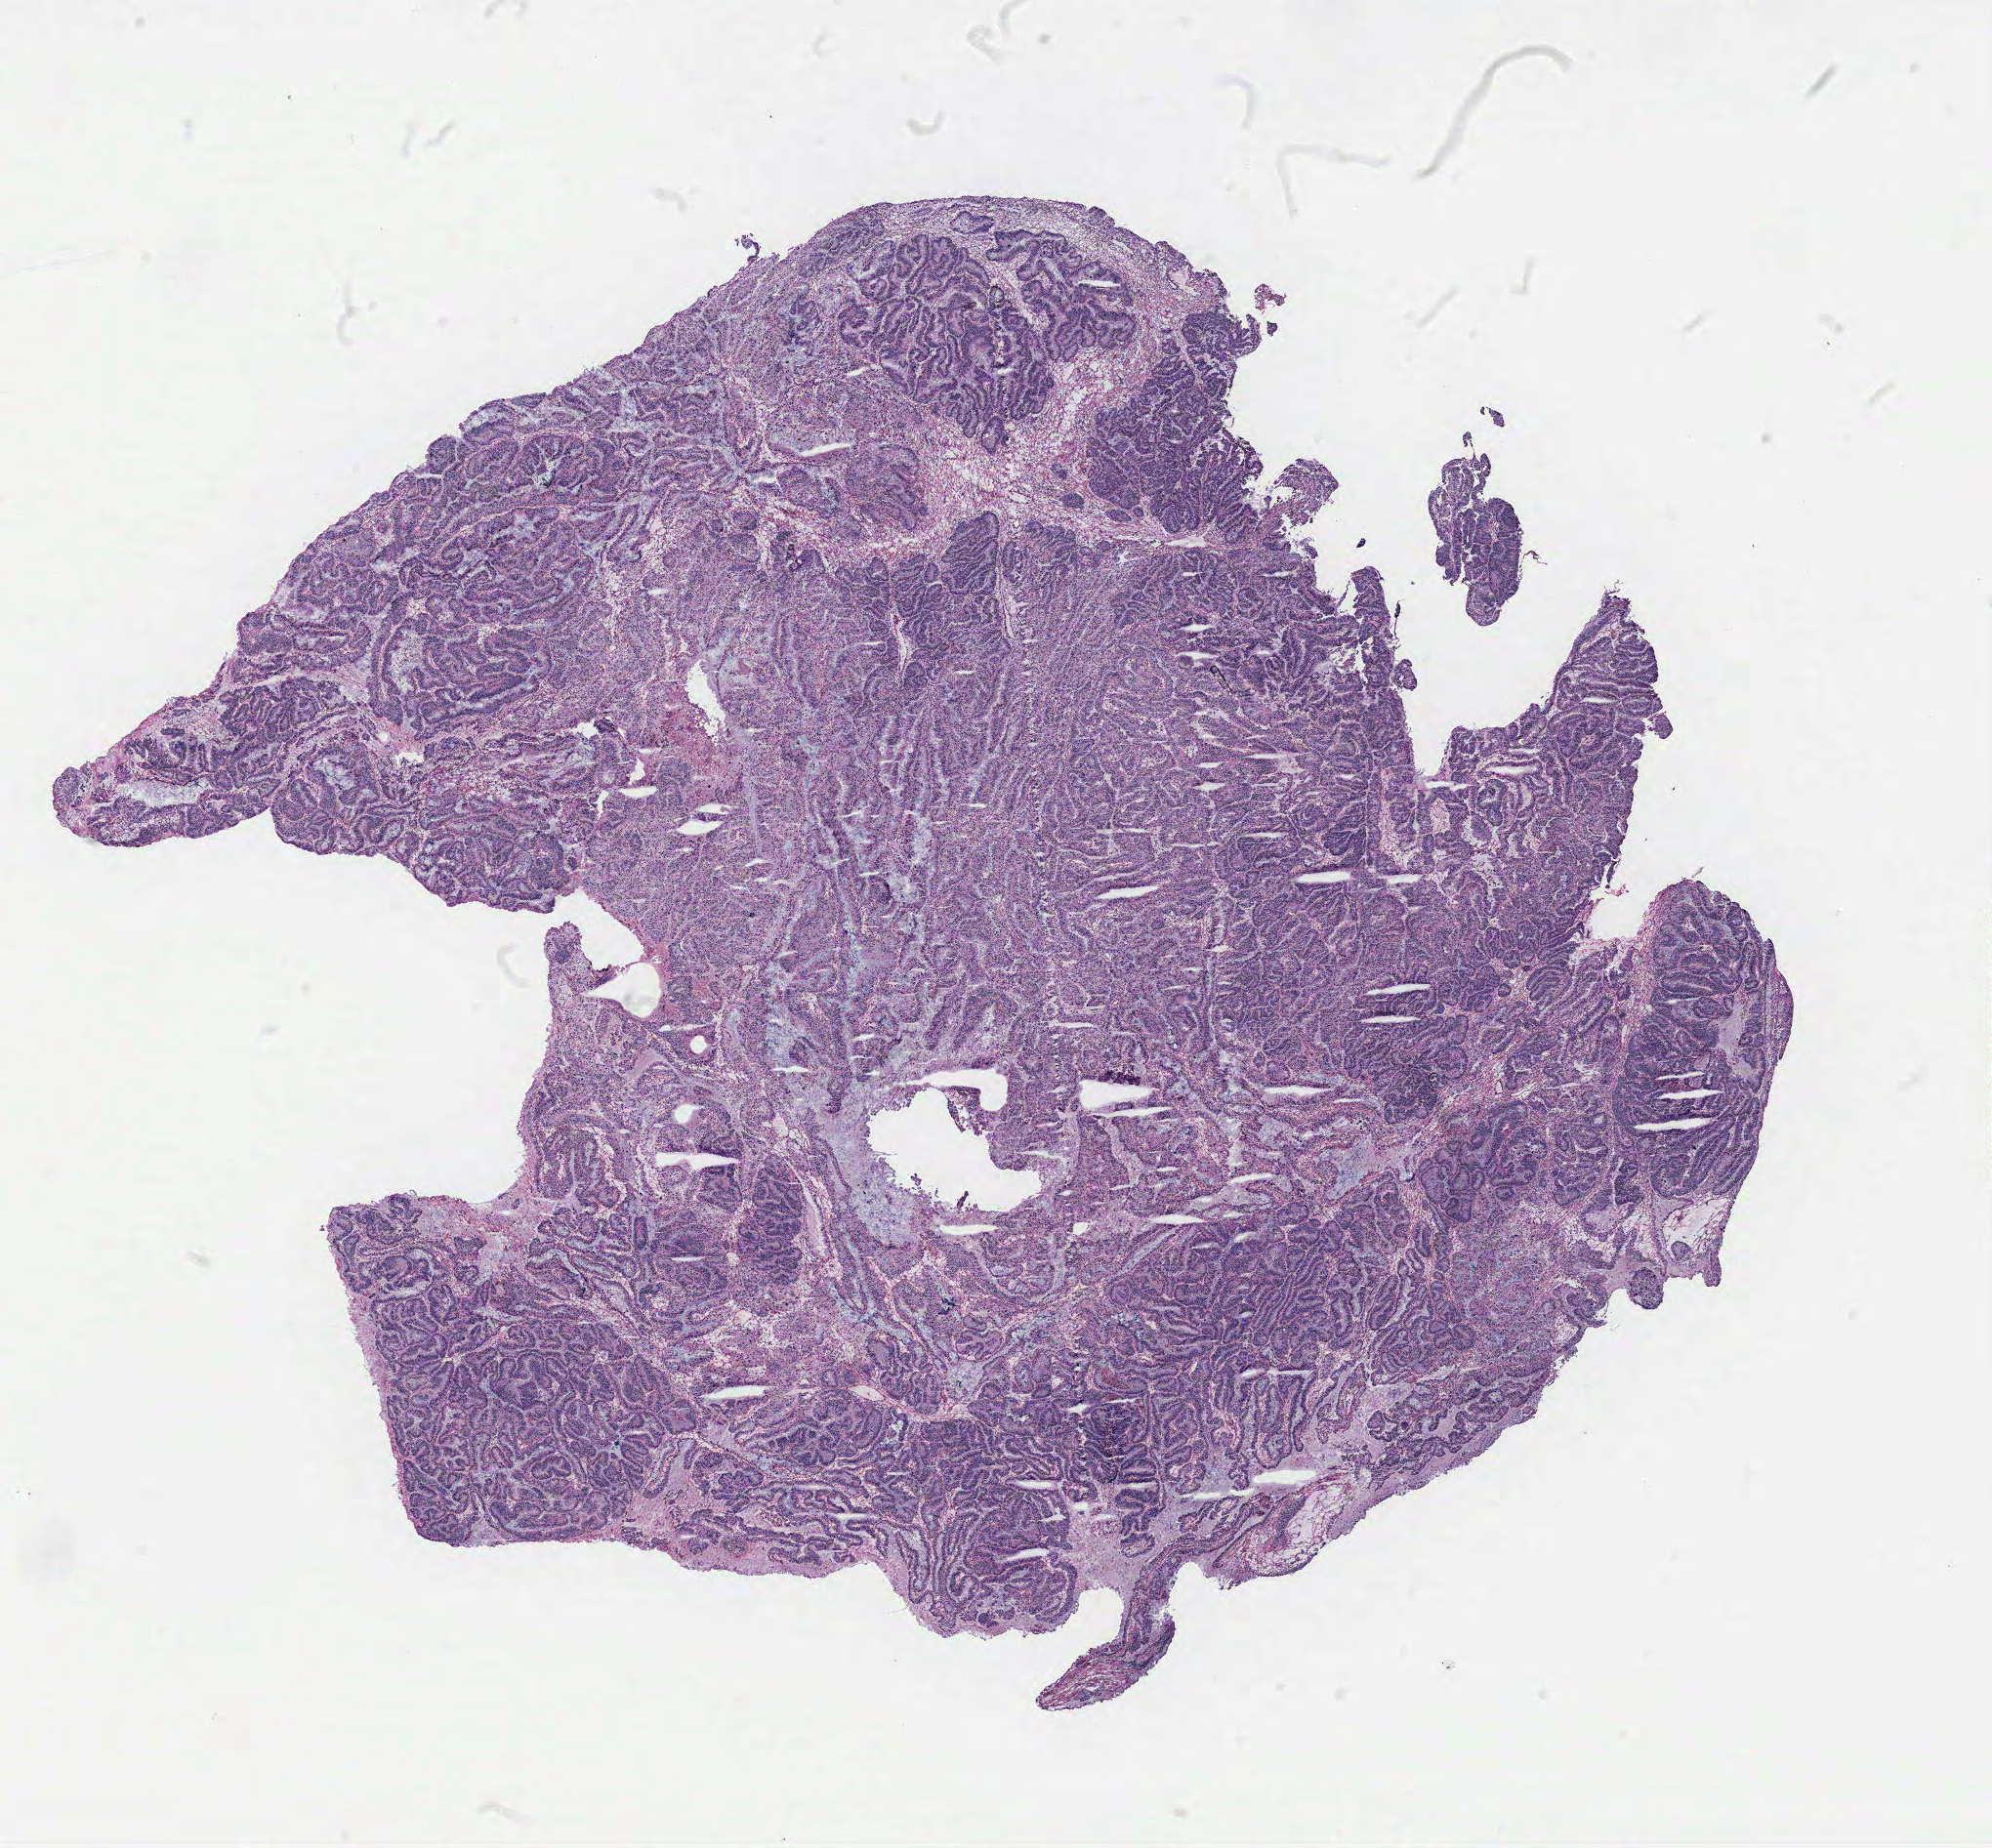
Whole-slide histology image, Hematoxylin and eosin (H&E) stained — whole scanned area (about 16.3 x 15.2 mm, slide scanned at 40x) shown as a low-resolution overview. Ovary, normal (non-tumour) tissue. Female, 48 y/o.
• this section: normal (non-tumour) tissue from the same patient
• patient diagnosis: Serous adenocarcinoma, NOS